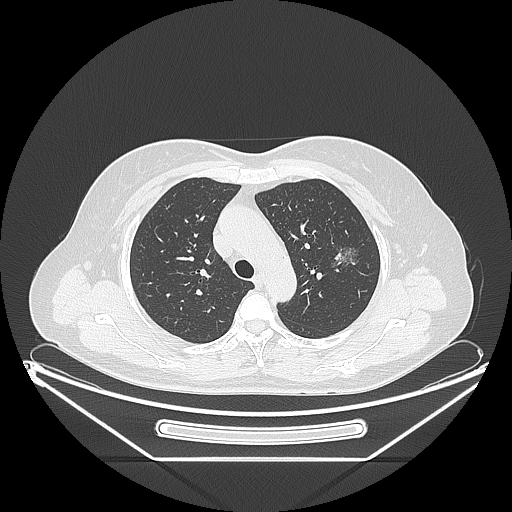
Chest CT, one axial slice; position 157 of 226 along the scan axis; lung window (W 1500 / L -600 HU); 1.25 mm slice thickness; 512 × 512 image matrix, field of view 447 × 447 mm. Female patient, age 54 years. From the clinical record (not read from this slice): clinical TNM (as recorded): T1c N0 M0; histopathological grade: G1.
Structures marked on this image (rectangle marked by the reading radiologist):
- lung tumour (recorded histology: adenocarcinoma): bounding box [x1, y1, x2, y2] px = [328, 238, 360, 271]